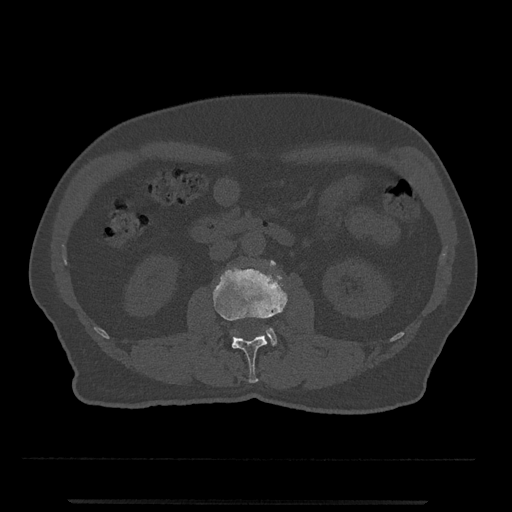
CT including the spine, one axial slice. Position 249 of 797 along the scan axis. Reconstruction kernel Br40s/3. 120 kVp. Bone window (W 1800 / L 400 HU). 0.5 mm slice thickness. 512 × 512 image matrix. Male patient, age 63 years. Case-level facts recorded for this patient, not image findings: primary cancer: prostate.
Structures marked on this image (semi-automatically segmented with operator editing):
- L2 vertebra: bounding box [x1, y1, x2, y2] px = [213, 261, 288, 383]
- L3 vertebra: [266, 260, 277, 346]